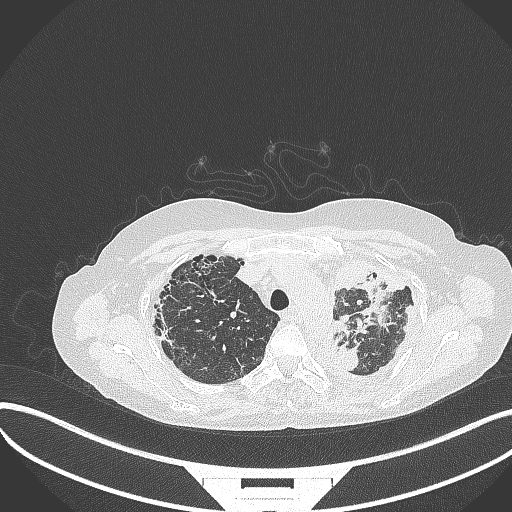
Chest CT, one axial slice. Position 265 of 373 along the scan axis. Lung window (W 1500 / L -600 HU). 1 mm slice thickness. 512 × 512 image matrix, field of view 400 × 400 mm. Female patient, age 56 years. Case-level facts recorded for this patient, not image findings: clinical TNM (as recorded): T1 N0 M0.
Structures marked on this image (bounding box drawn by a radiologist):
- lung tumour (recorded histology: adenocarcinoma): box from (x=330, y=333) to (x=368, y=370) px
- lung tumour (recorded histology: adenocarcinoma): (x=358, y=255)–(x=400, y=326)